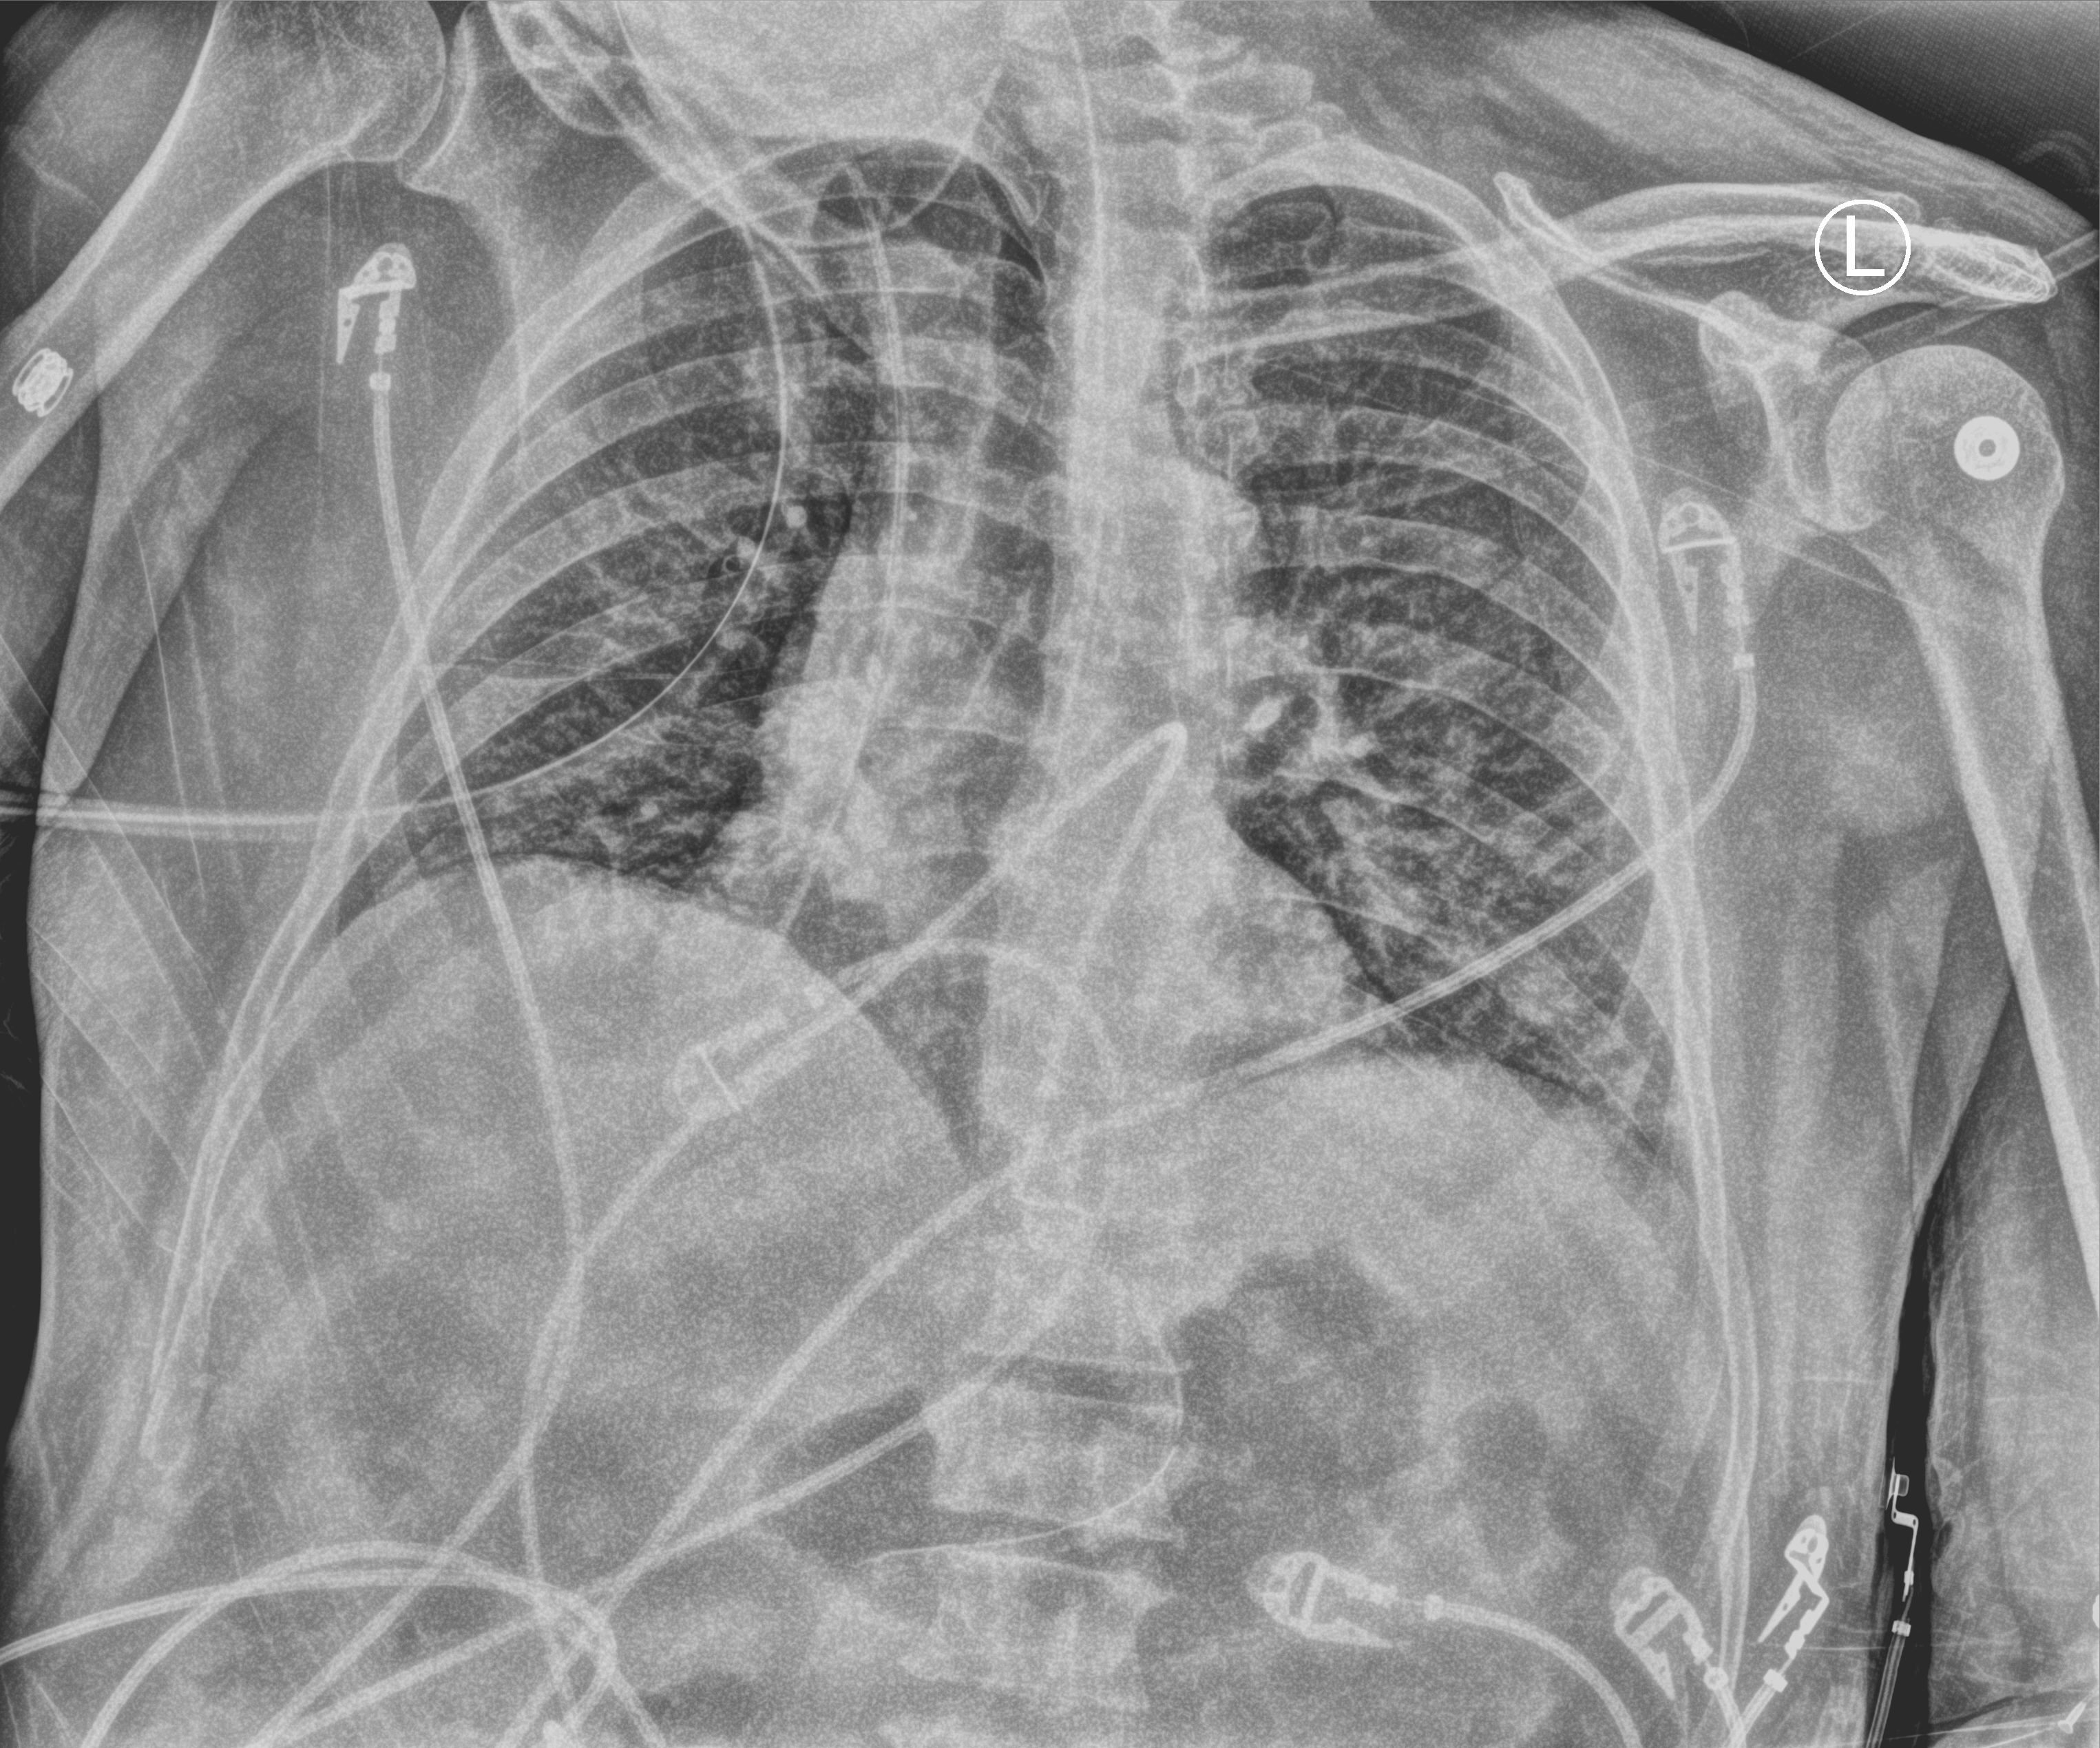
Bedside chest radiograph (computed radiography), anteroposterior (AP) projection. Male patient hospitalised with COVID-19, age 18–59 years.
Hospital-stay facts (about this admission, not read from this image; timing relative to this image not recorded): admitted to intensive care during this hospital stay: yes.